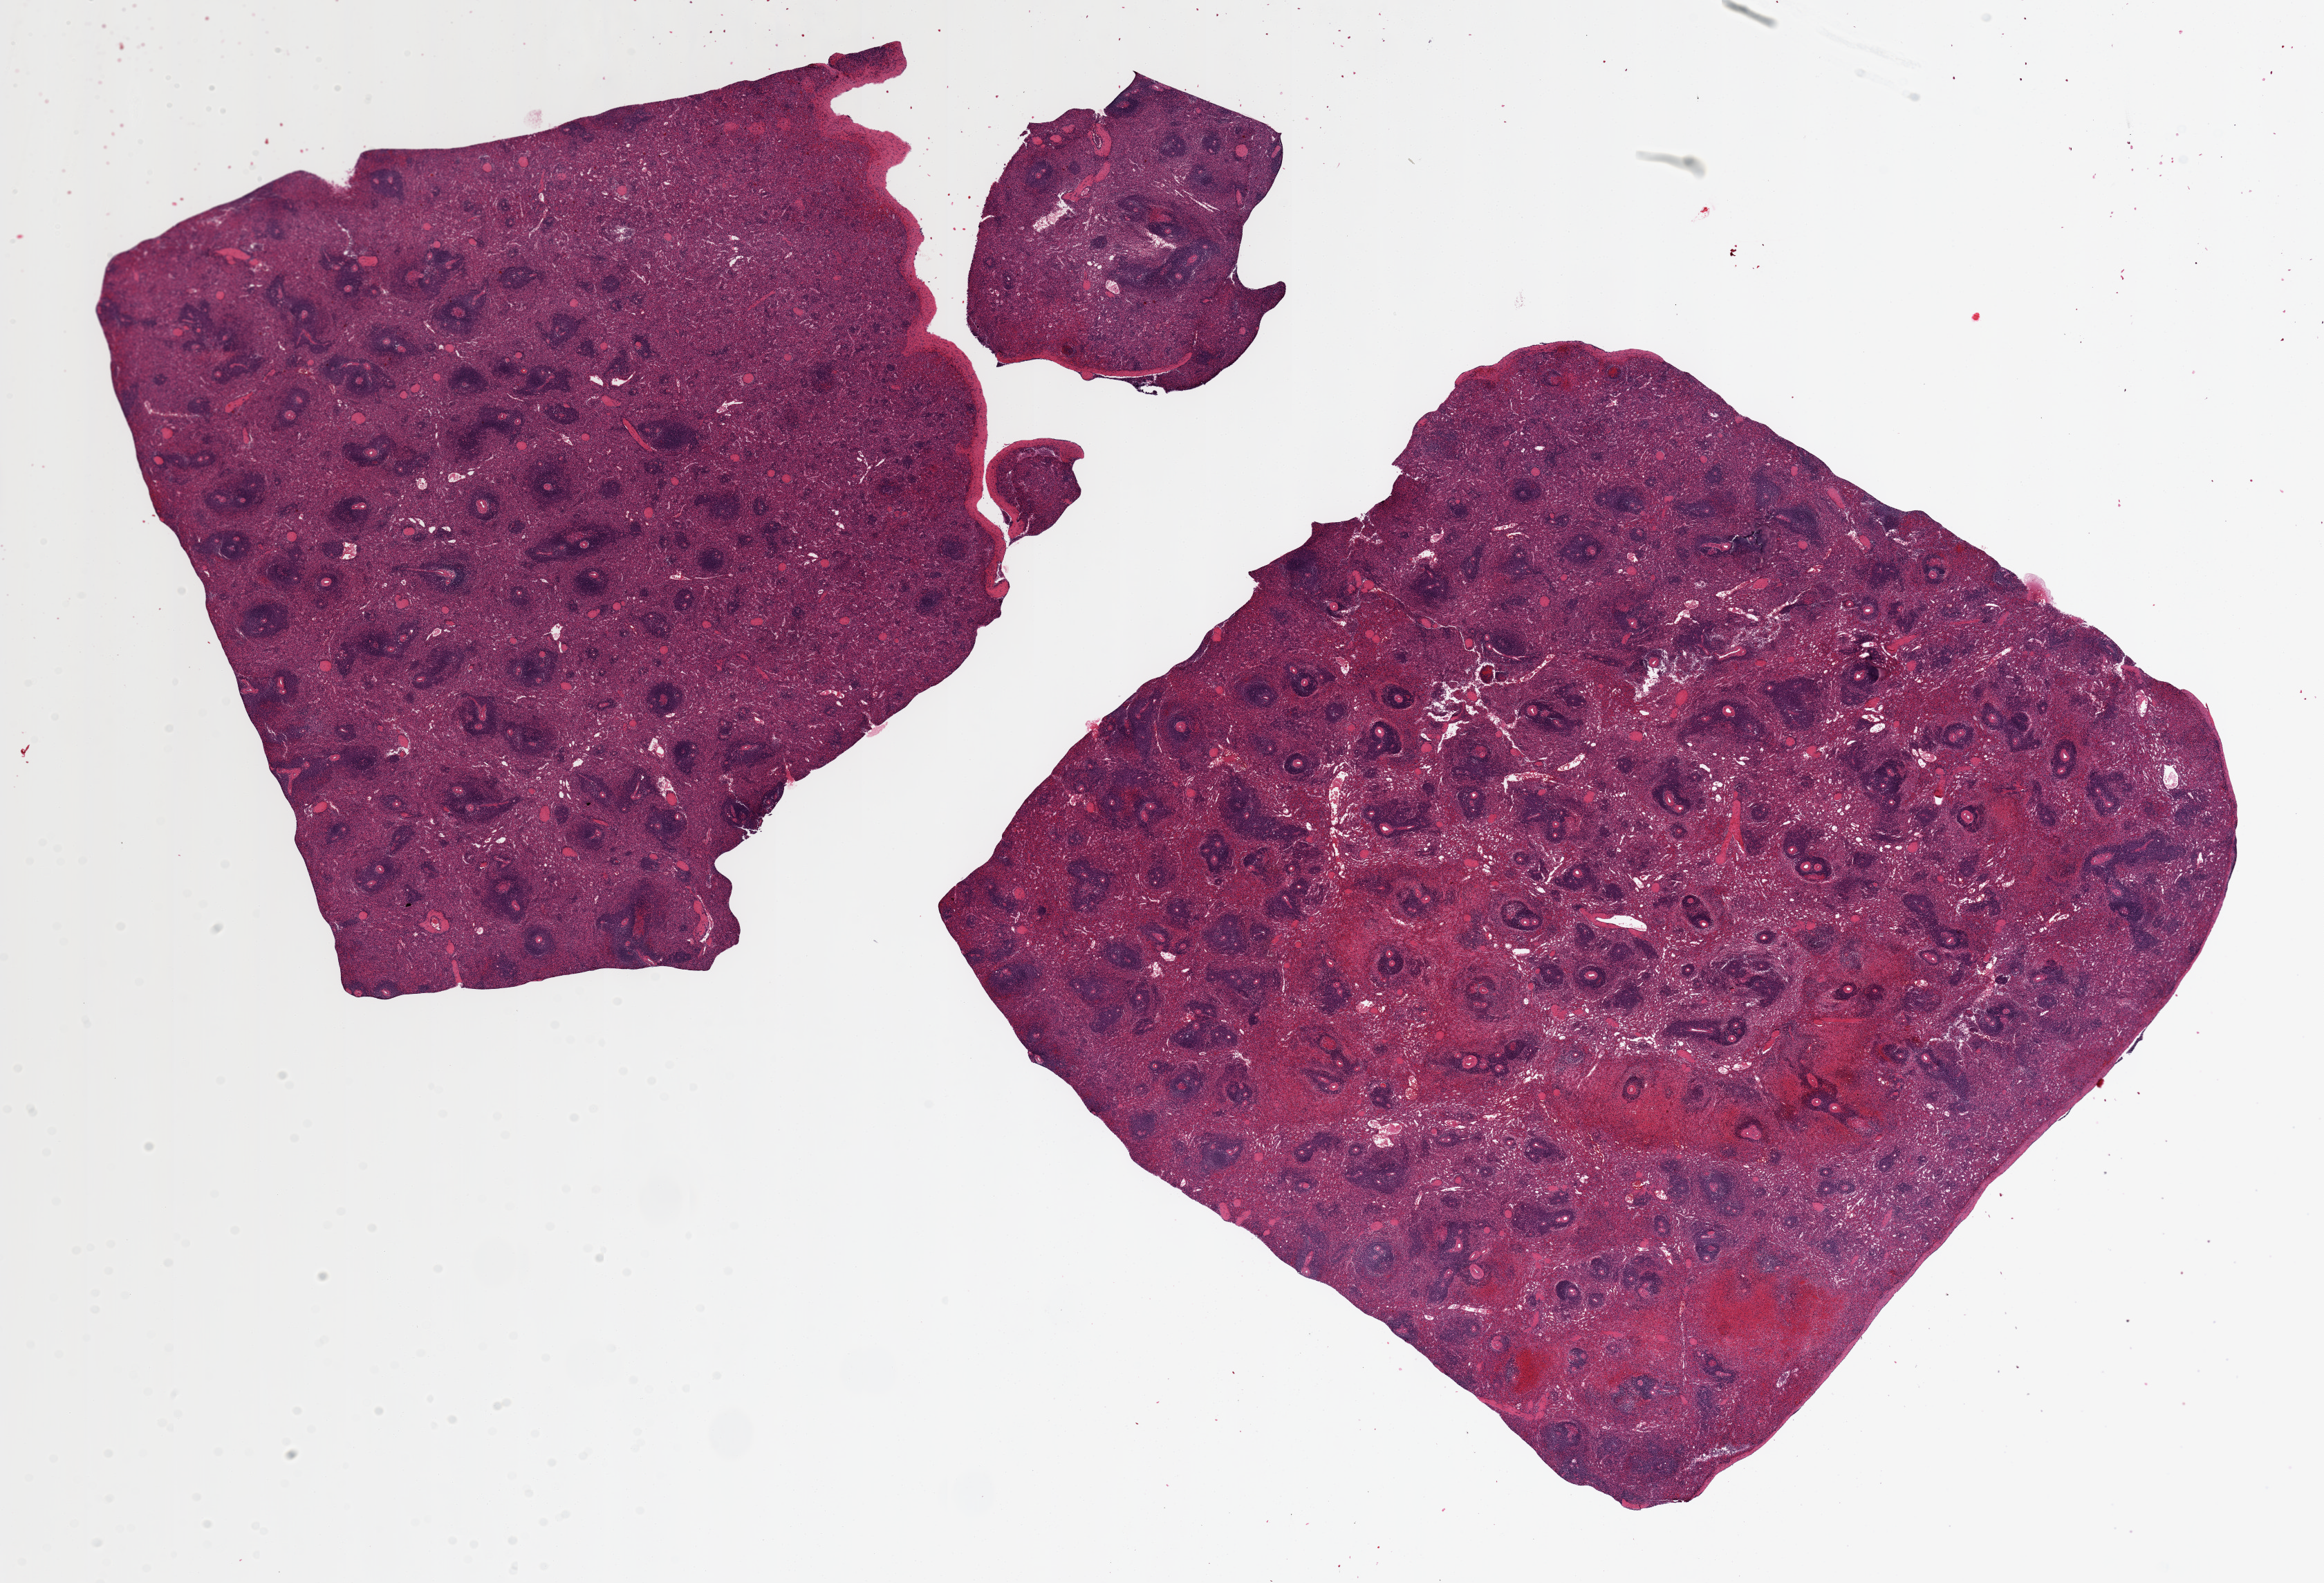
Digitized H&E-stained section, shown as a low-resolution overview of the whole scanned area (about 26.6 x 18.1 mm), PAXgene-fixed paraffin-embedded (PFPE) section, section of spleen (target tissue), tissue donor sample. Donor sex: female.
Review note (as recorded): 2 ~10mmx10mm aliquots, central under-fixation with holes/tears.